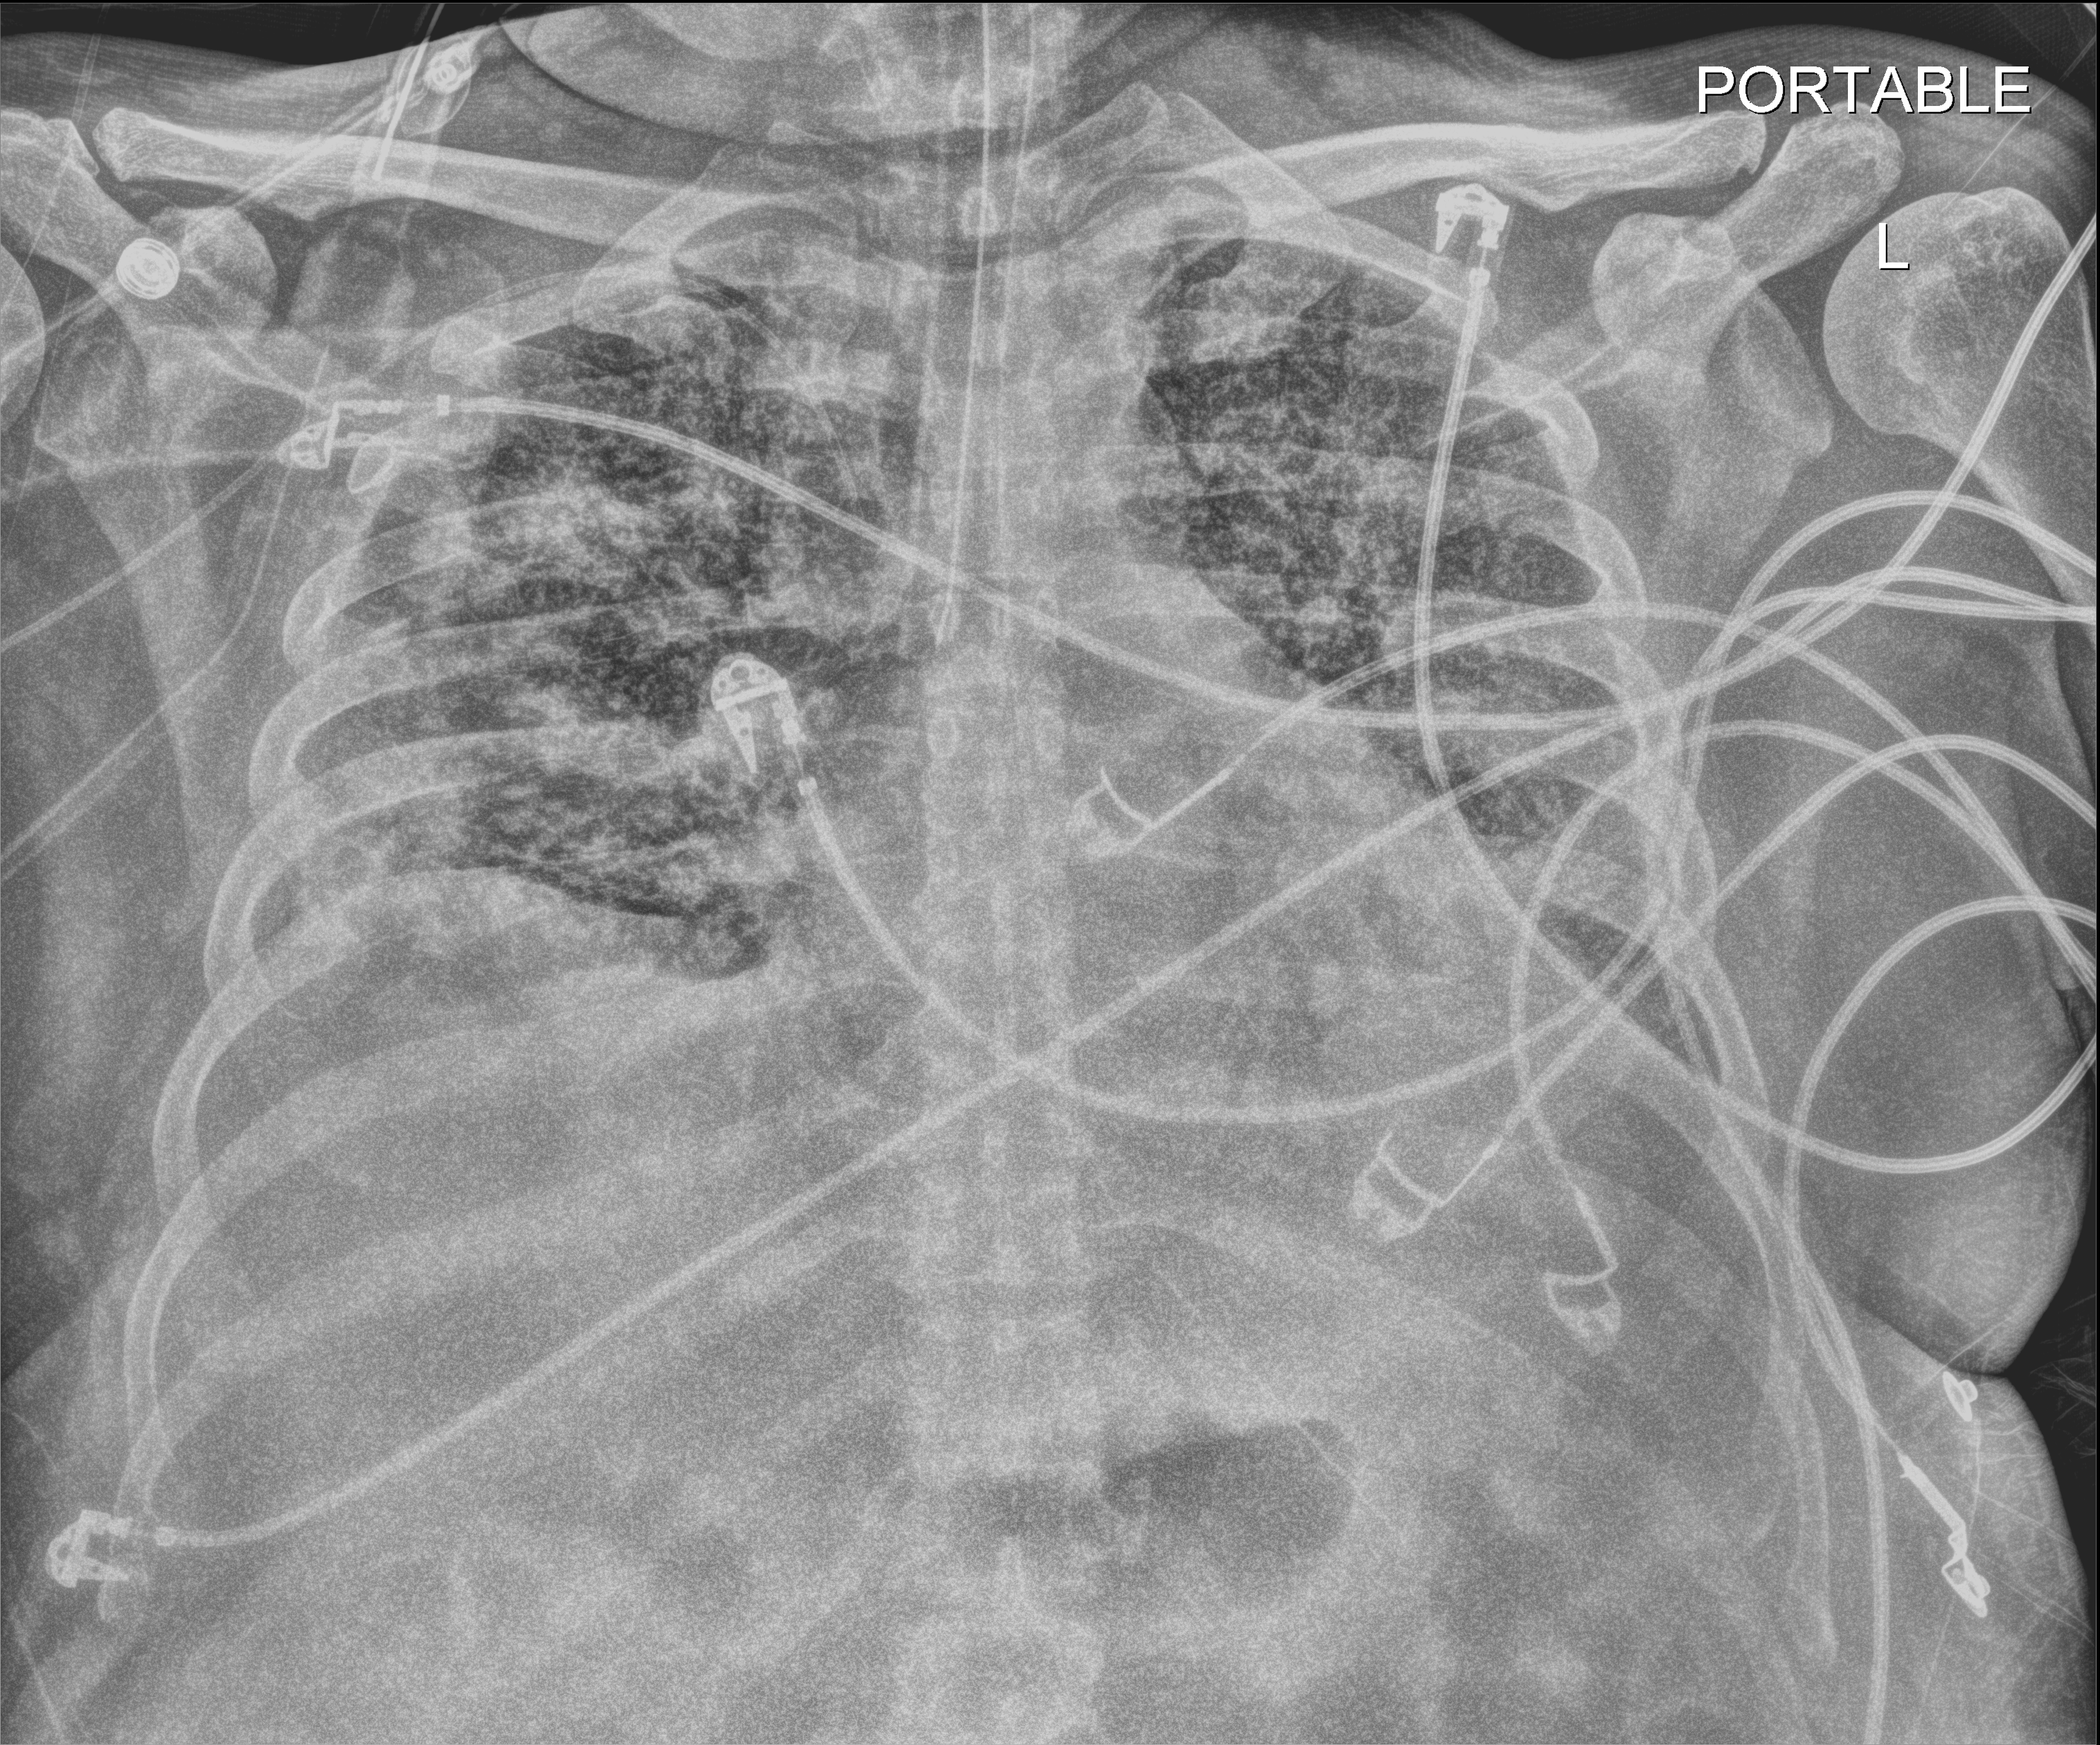
Chest X-ray (portable); anteroposterior (AP) projection. Male patient hospitalised with COVID-19, age 18–59 years.
Hospital-stay facts (about this admission, not read from this image; timing relative to this image not recorded): admitted to intensive care during this hospital stay: yes; mechanically ventilated during this hospital stay: yes; diabetes (admission record): no.